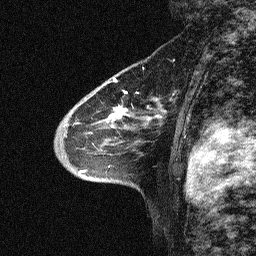
Breast MRI (dynamic contrast-enhanced), one sagittal slice. Position 42 of 64 along the scan axis. Dynamic contrast-enhanced study with each time point stored as its own series, time point 2 of 3 at this slice position (early post-contrast, ordered by acquisition time). 1.5 T. TE 4.5 ms, TR 11 ms. 2.06 mm slice thickness. 256 × 256 image matrix, field of view 200 × 200 mm. Patient: female, 46 years. From the clinical record (not read from this slice): setting: breast cancer imaged before/during neoadjuvant chemotherapy; receptor status: HER2-positive.
Structures marked on this image (semi-automatic segmentation, software-assisted and operator-edited):
- analysis volume of interest (the breast-tissue region the enhancement analysis was run in; not a lesion): bounding box [x1, y1, x2, y2] px = [46, 51, 180, 169]
- tumour enhancement mask (voxels above the 90 % enhancement threshold inside the analysis volume of interest): [109, 107, 124, 119]